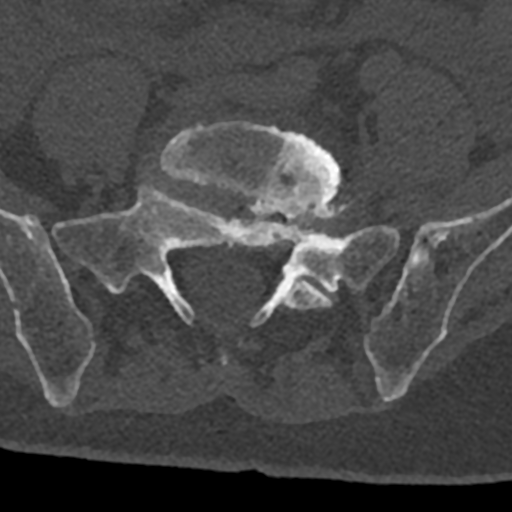
CT including the spine, one axial slice; position 170 of 797 along the scan axis; reconstruction kernel Br40s/3; 120 kVp; bone window (W 1800 / L 400 HU); 512 × 512 image matrix, field of view 160 × 160 mm. Male patient, age 74 years. From the clinical record (not read from this slice): primary cancer: renal.
Outlined on this slice (semi-automatic segmentation, software-assisted and operator-edited):
- L5 vertebra: bounding box [x1, y1, x2, y2] px = [159, 121, 340, 366]